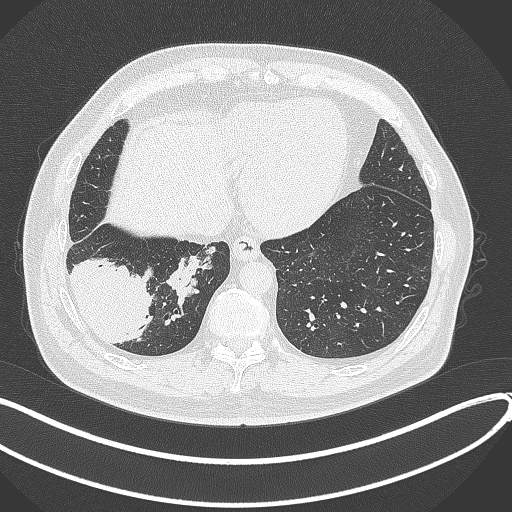
Chest CT, one axial slice. Slice 85 of 360 in the series (ordered by position). Lung window (W 1500 / L -600 HU). 512 × 512 image matrix, field of view 400 × 400 mm. Male patient, age 59 years.
Structures marked on this image (bounding box drawn by a radiologist):
- lung tumour (recorded histology: adenocarcinoma): bounding box [x1, y1, x2, y2] px = [67, 251, 157, 348]